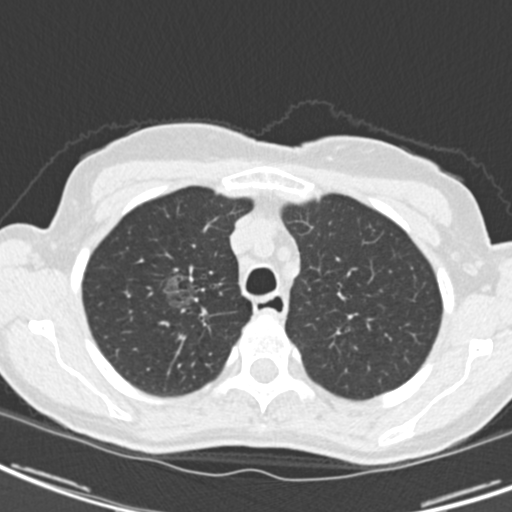
Low-dose screening chest CT, one axial slice. Position 156 of 189 along the scan axis. Reconstruction kernel B30f. 120 kVp. Lung window (W 1500 / L -600 HU). 2 mm slice thickness. 512 × 512 image matrix, field of view 279 × 279 mm.
Structures marked on this image (manually delineated by an expert):
- lesion 1 (tumor, upper lobe of right lung): box from (x=162, y=274) to (x=200, y=310) px